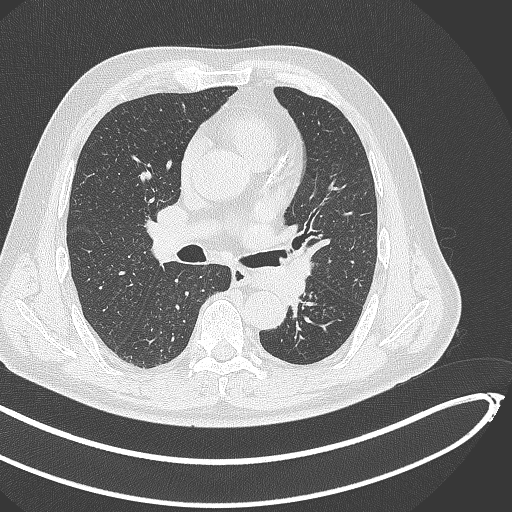
Chest CT, one axial slice; position 262 of 468 along the scan axis; lung window (W 1500 / L -600 HU); 512 × 512 image matrix, field of view 400 × 400 mm. Patient: male, 64 years. Case-level facts recorded for this patient, not image findings: clinical TNM (as recorded): T1c N0 M0; histopathological grade: G2.
Outlined on this slice (rectangle marked by the reading radiologist):
- lung tumour (recorded histology: squamous cell carcinoma): bounding box <248,255,318,304> (left, top, right, bottom; pixels)